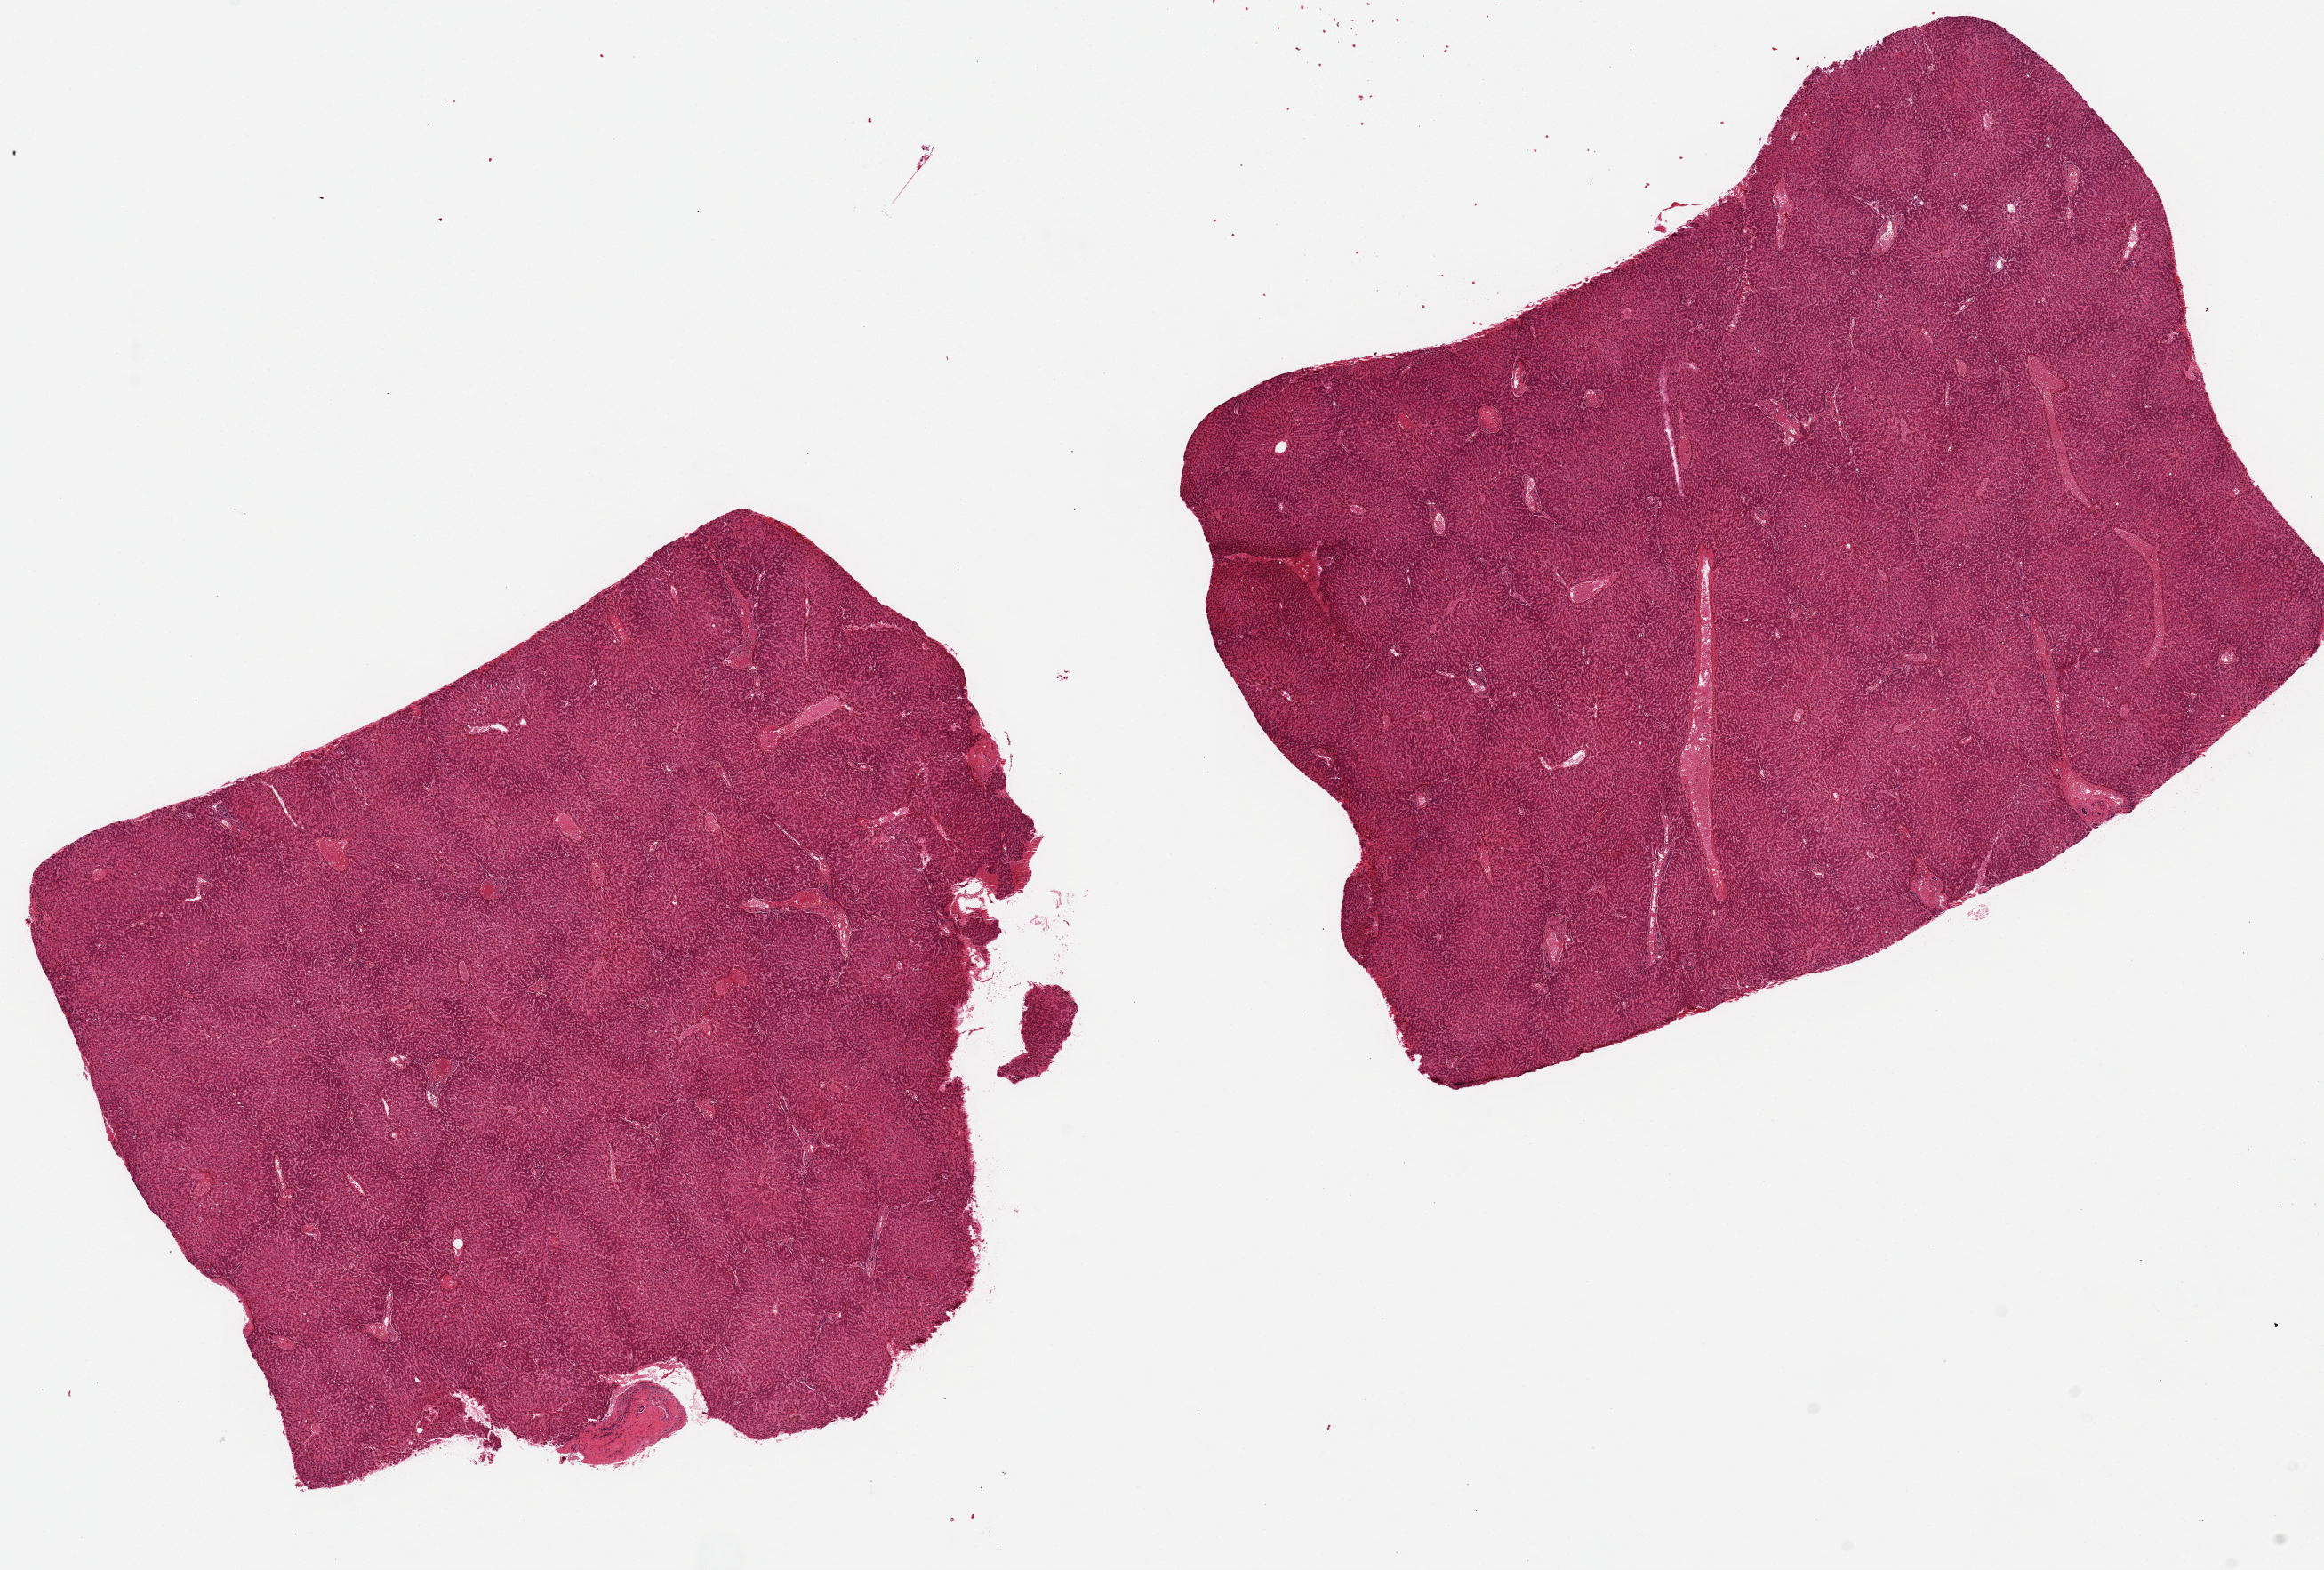
Haematoxylin and eosin whole-slide image — whole scanned area (about 20.7 x 14.0 mm, acquisition: 20x scan) shown as a low-resolution overview. PAXgene-fixed, paraffin-embedded tissue. Sampled site (target tissue): liver. Tissue donor sample. Donor sex: male.
• reviewer comment on this tissue sample: 2 ~8x8mm aliquots, prominent congestion